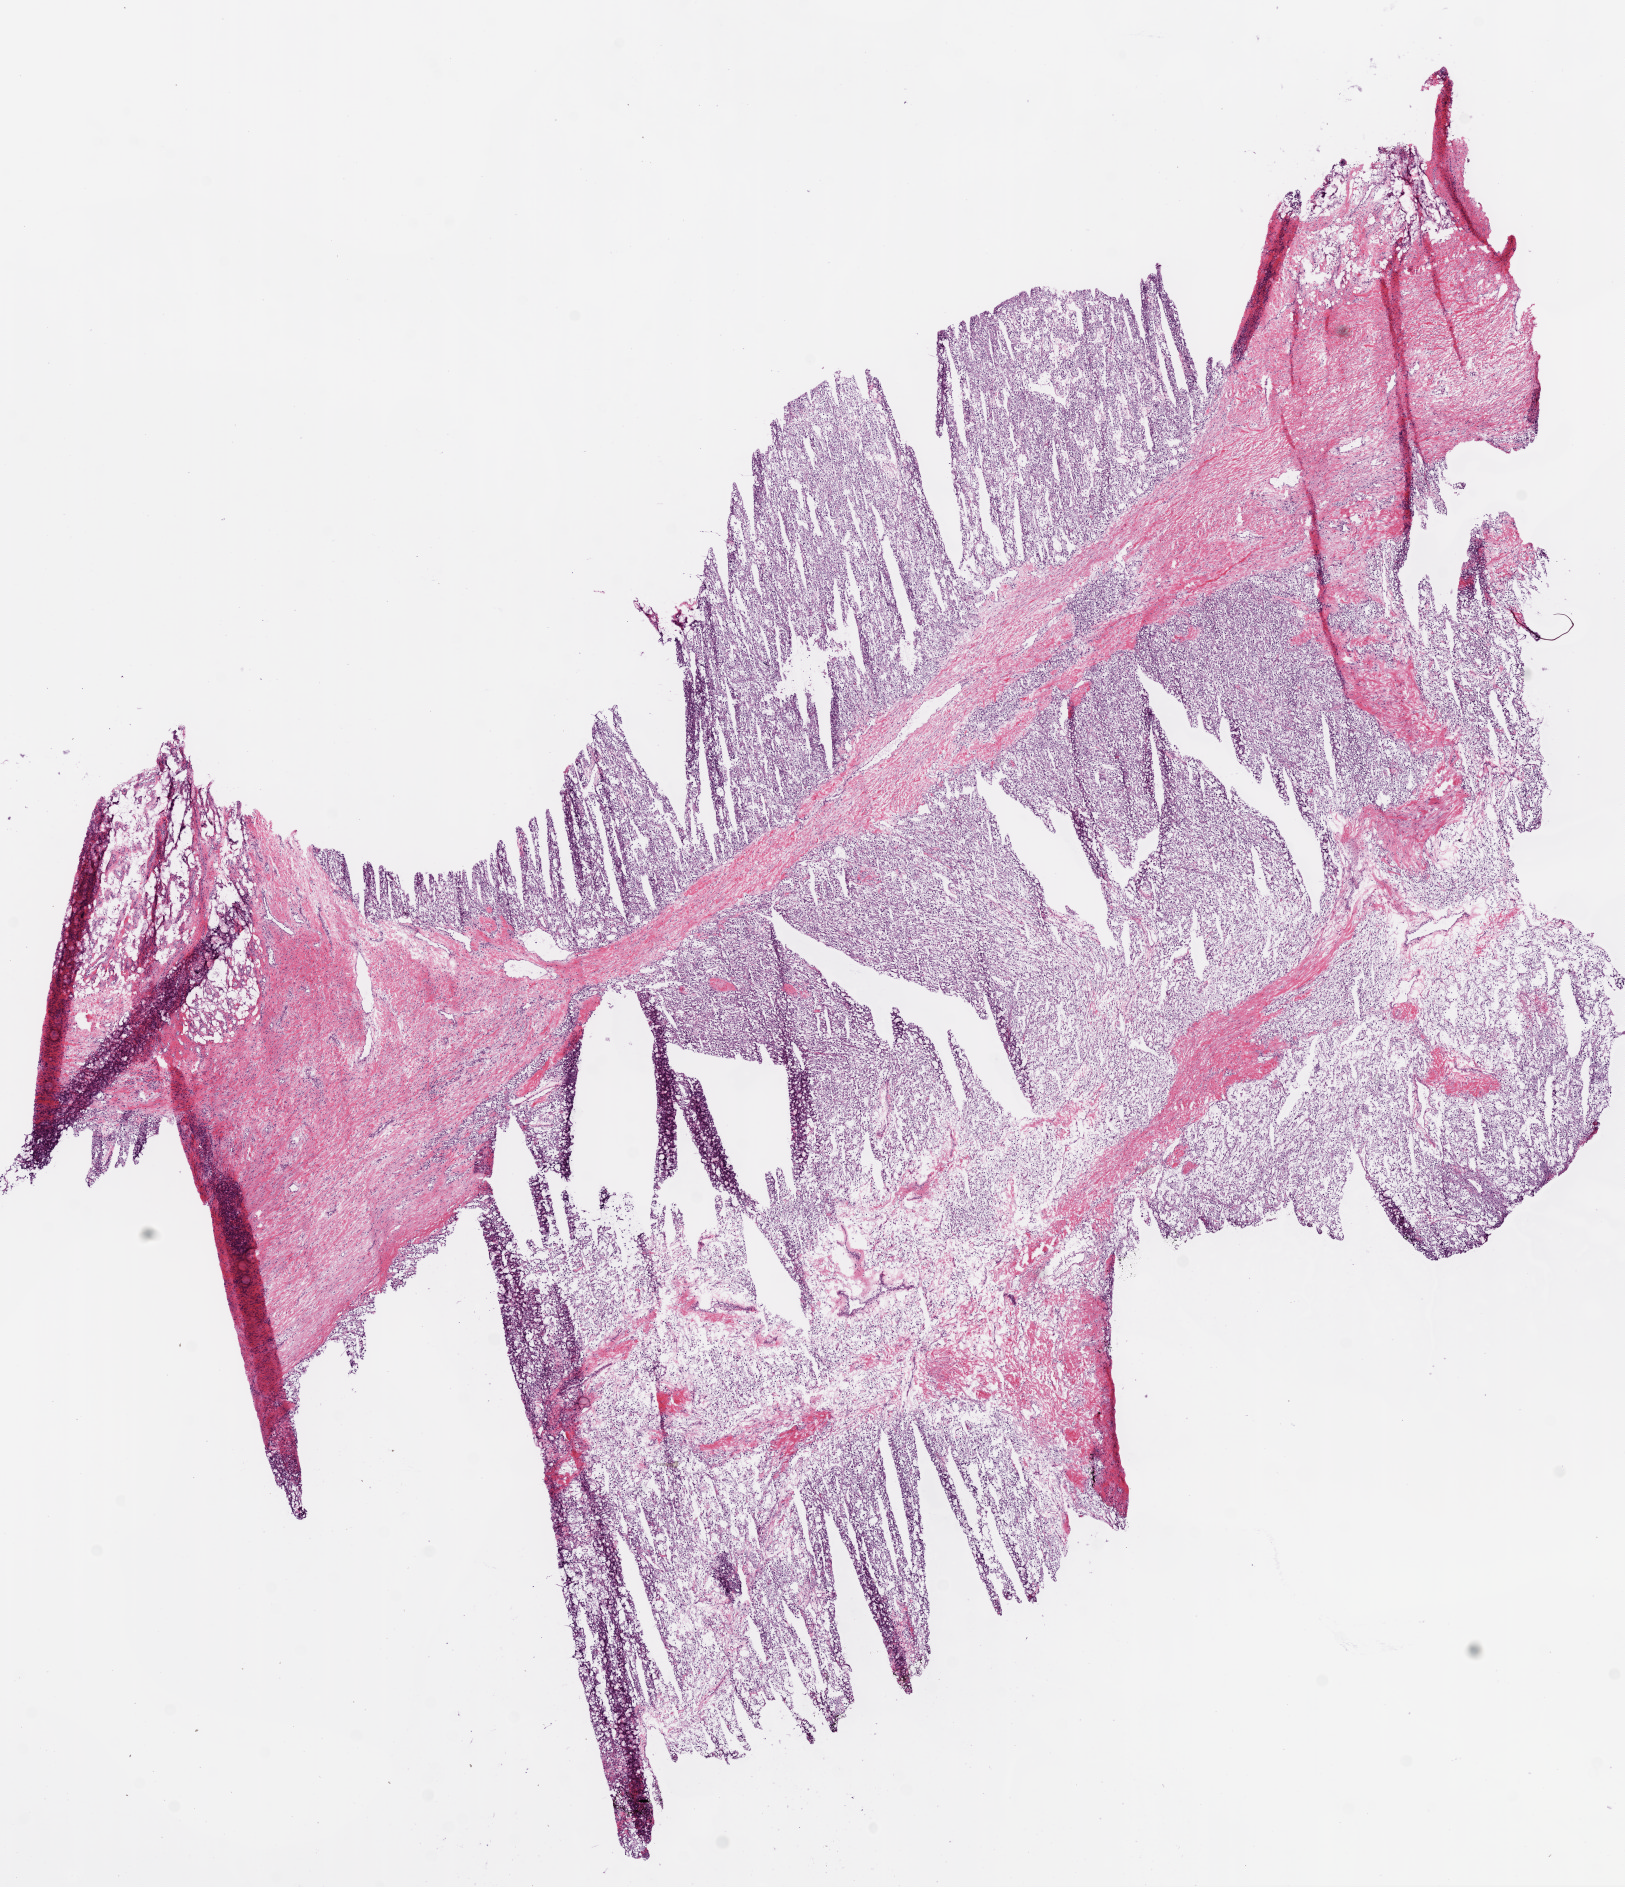
Hematoxylin and eosin (H&E) stained whole-slide image, a low-resolution overview of the entire scanned area, about 13.0 x 15.1 mm (slide scanned at 20x). Frozen section from the bottom of the tissue portion. Sample: primary tumour, kidney. Male, age 57 years at initial diagnosis.
Diagnosis: Clear cell adenocarcinoma, NOS.